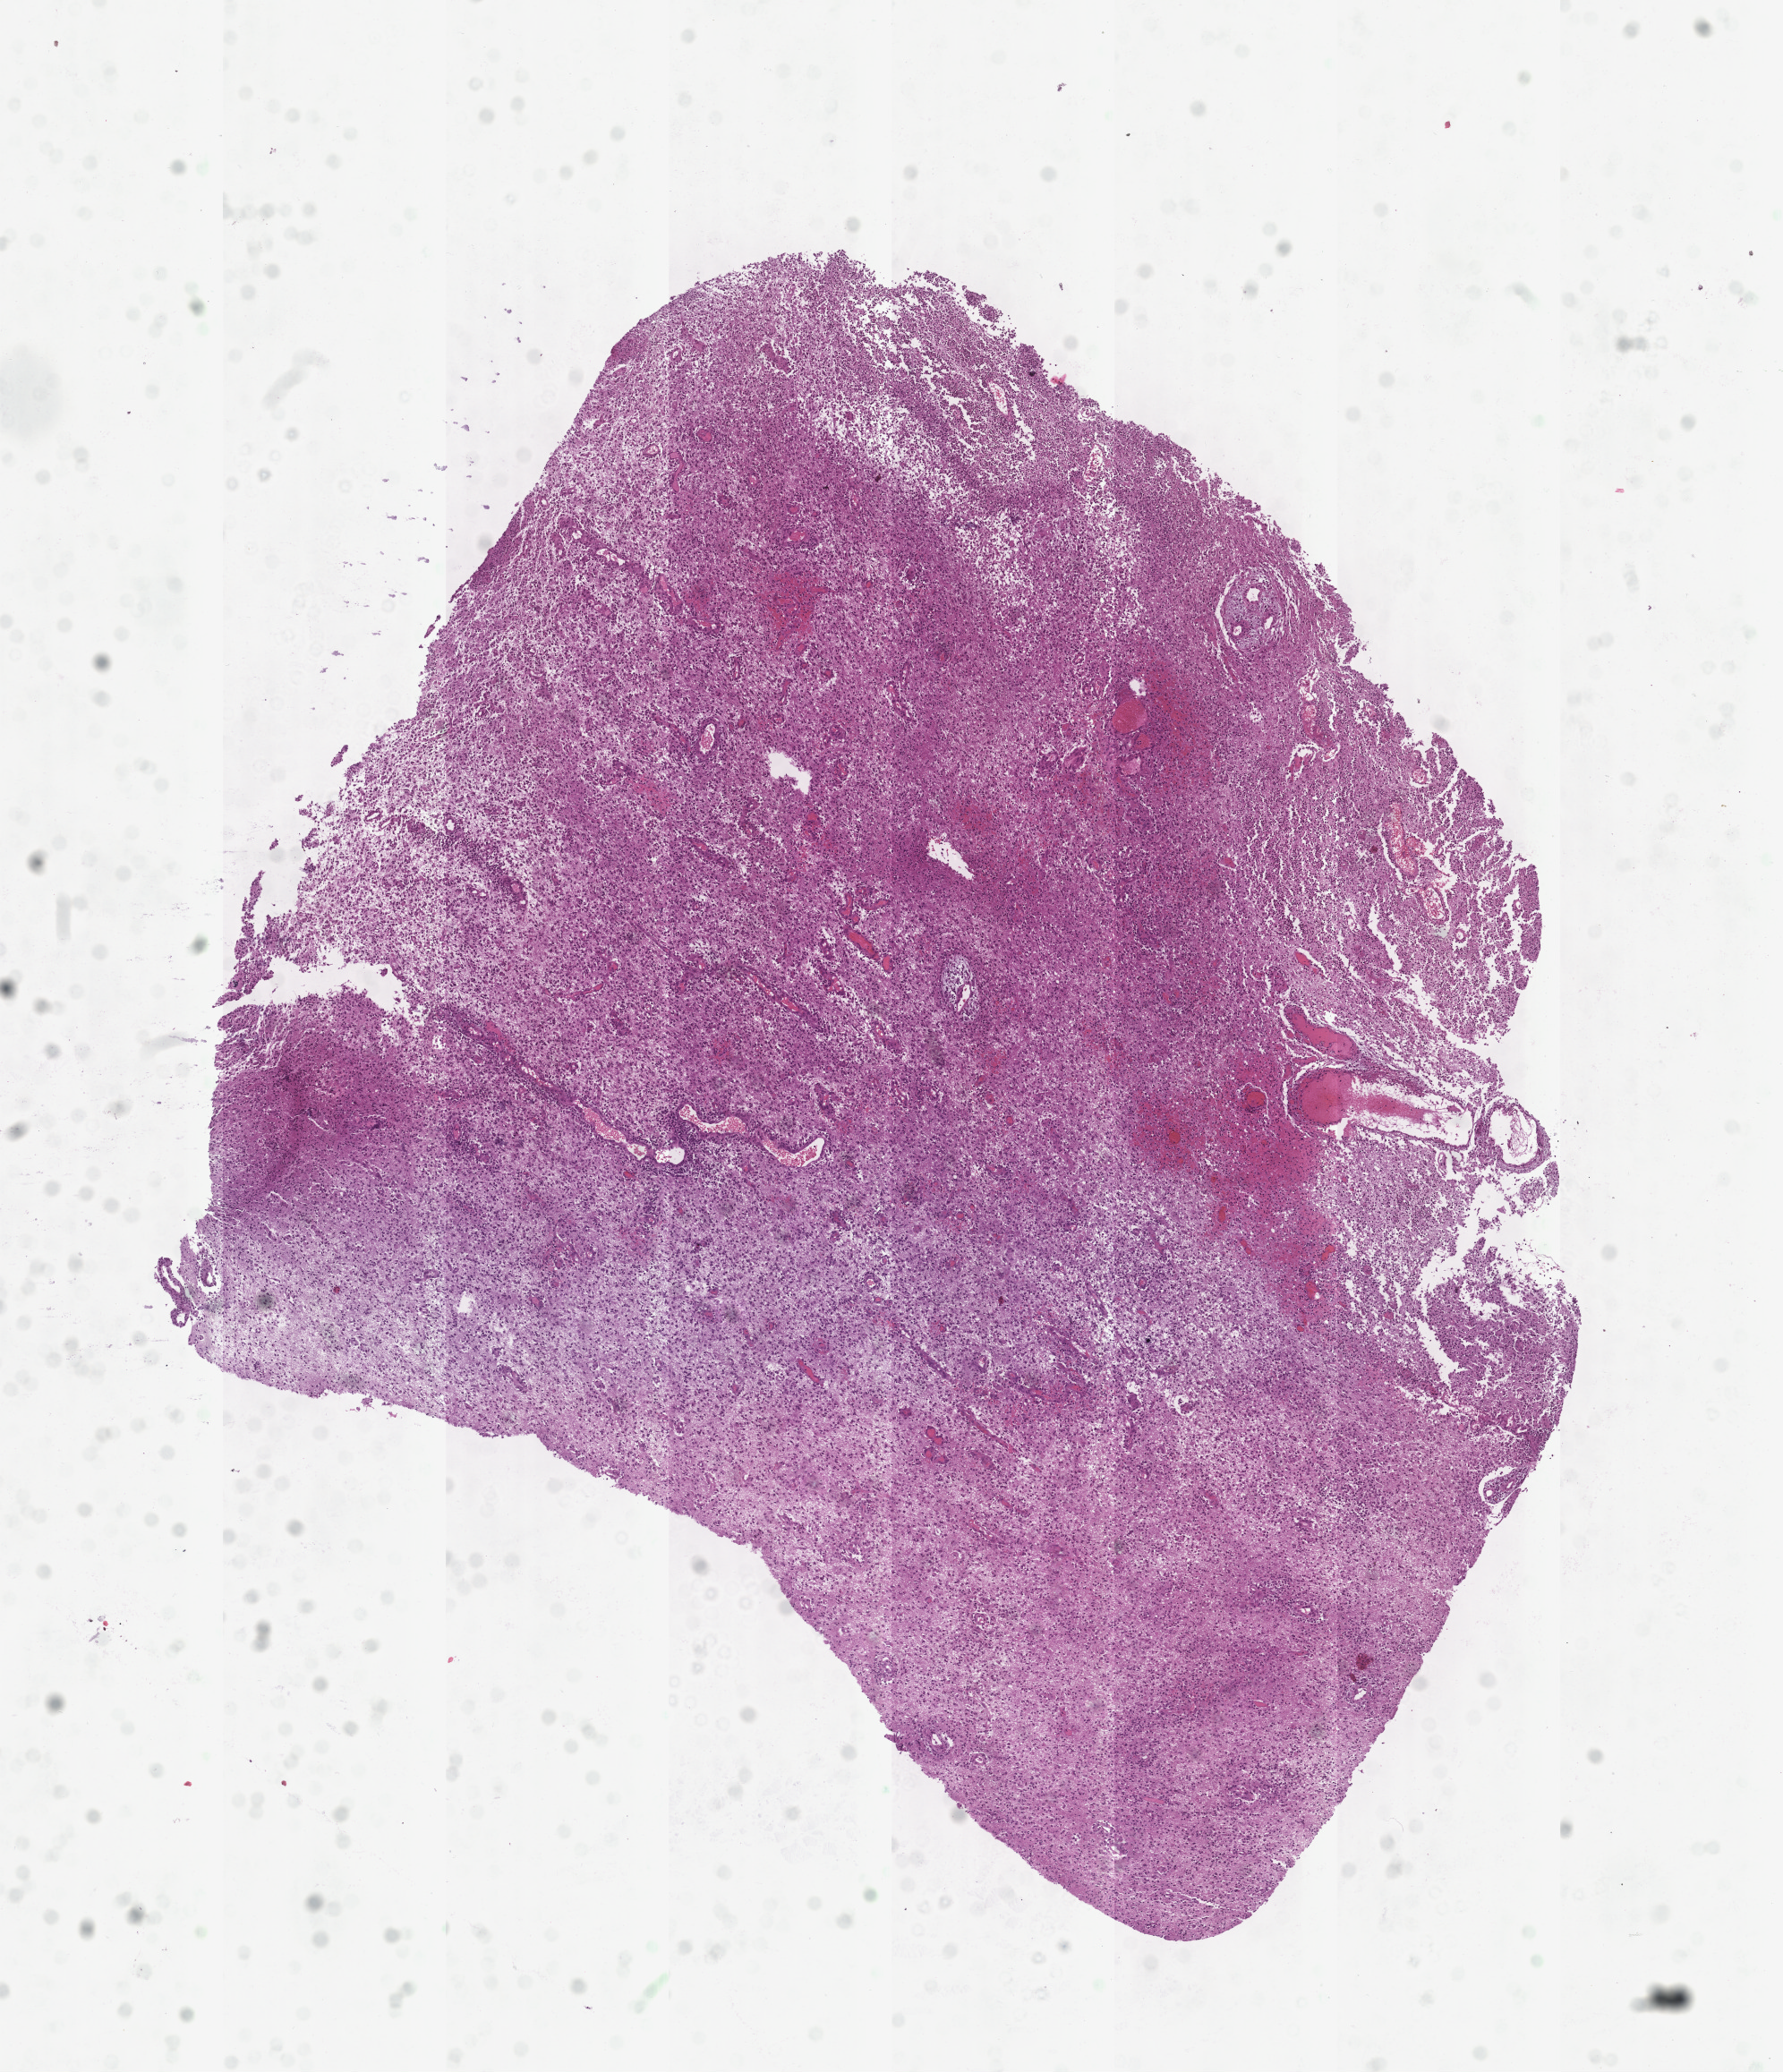
H&E-stained whole-slide image — whole scanned area (about 8.0 x 9.3 mm, from a 20x scan) shown as a low-resolution overview, brain, tumour tissue. Patient: male, age 39 years.
Histologic diagnosis: Glioblastoma.